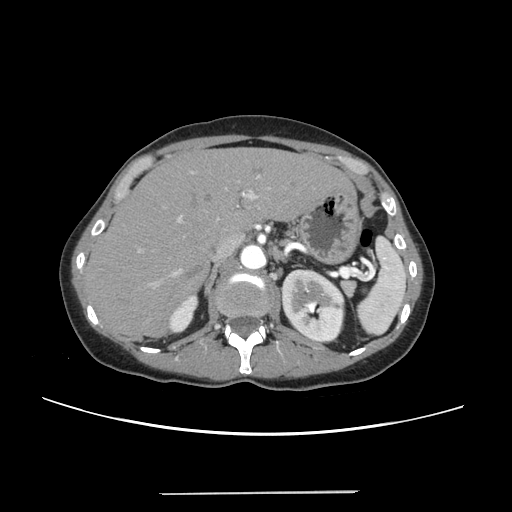
Contrast-enhanced abdominal CT, one axial slice; slice 165 of 240 in the series (ordered by position); 120 kVp; intravenous contrast given; soft-tissue window (W 400 / L 40 HU); 512 × 512 image matrix, field of view 371 × 371 mm. Female patient, age 60 years. Case-level facts recorded for this patient, not image findings: diagnosis: colorectal cancer liver metastases, imaged before liver resection; multiple liver metastases: no.
Annotated regions visible in this slice (manually delineated by an expert):
- liver: box from (x=87, y=148) to (x=348, y=336) px
- planned liver remnant (the part of the liver to remain after resection): (x=87, y=148)–(x=347, y=335)
- portal vein (with intrahepatic branches): (x=138, y=172)–(x=259, y=287)